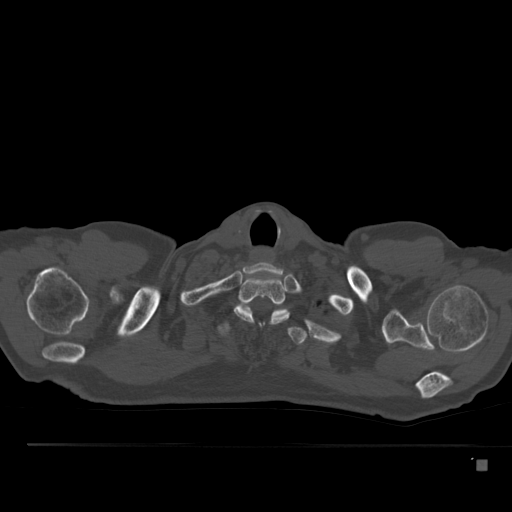
CT including the spine, one axial slice; position 423 of 517 along the scan axis; 120 kVp; bone window (W 1800 / L 400 HU); 1.5 mm slice thickness; 512 × 512 image matrix, field of view 408 × 408 mm. Patient: male, 70 years. Case-level facts recorded for this patient, not image findings: primary cancer: renal; vertebrae with lytic lesions (as recorded): T4, T6, T10, T12, L3, L4, L5.
Structures marked on this image (semi-automatically segmented with operator editing):
- T1 vertebra: bounding box [x1, y1, x2, y2] px = [234, 275, 290, 327]
- T2 vertebra: [217, 301, 308, 345]